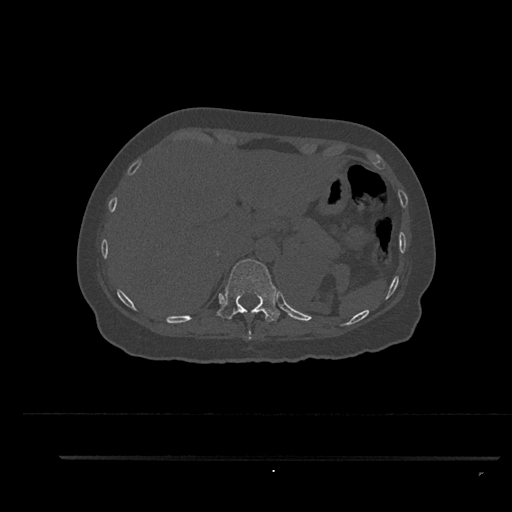
CT including the spine, one axial slice. Position 325 of 797 along the scan axis. 120 kVp. Bone window (W 1800 / L 400 HU). 512 × 512 image matrix, field of view 408 × 408 mm. Patient: female, 44 years. Case-level facts recorded for this patient, not image findings: primary cancer: renal; vertebrae with lytic lesions (as recorded): L1.
Structures marked on this image (semi-automatically segmented with operator editing):
- T10 vertebra: bounding box <248,329,252,340> (left, top, right, bottom; pixels)
- T11 vertebra: <216,259,280,322>